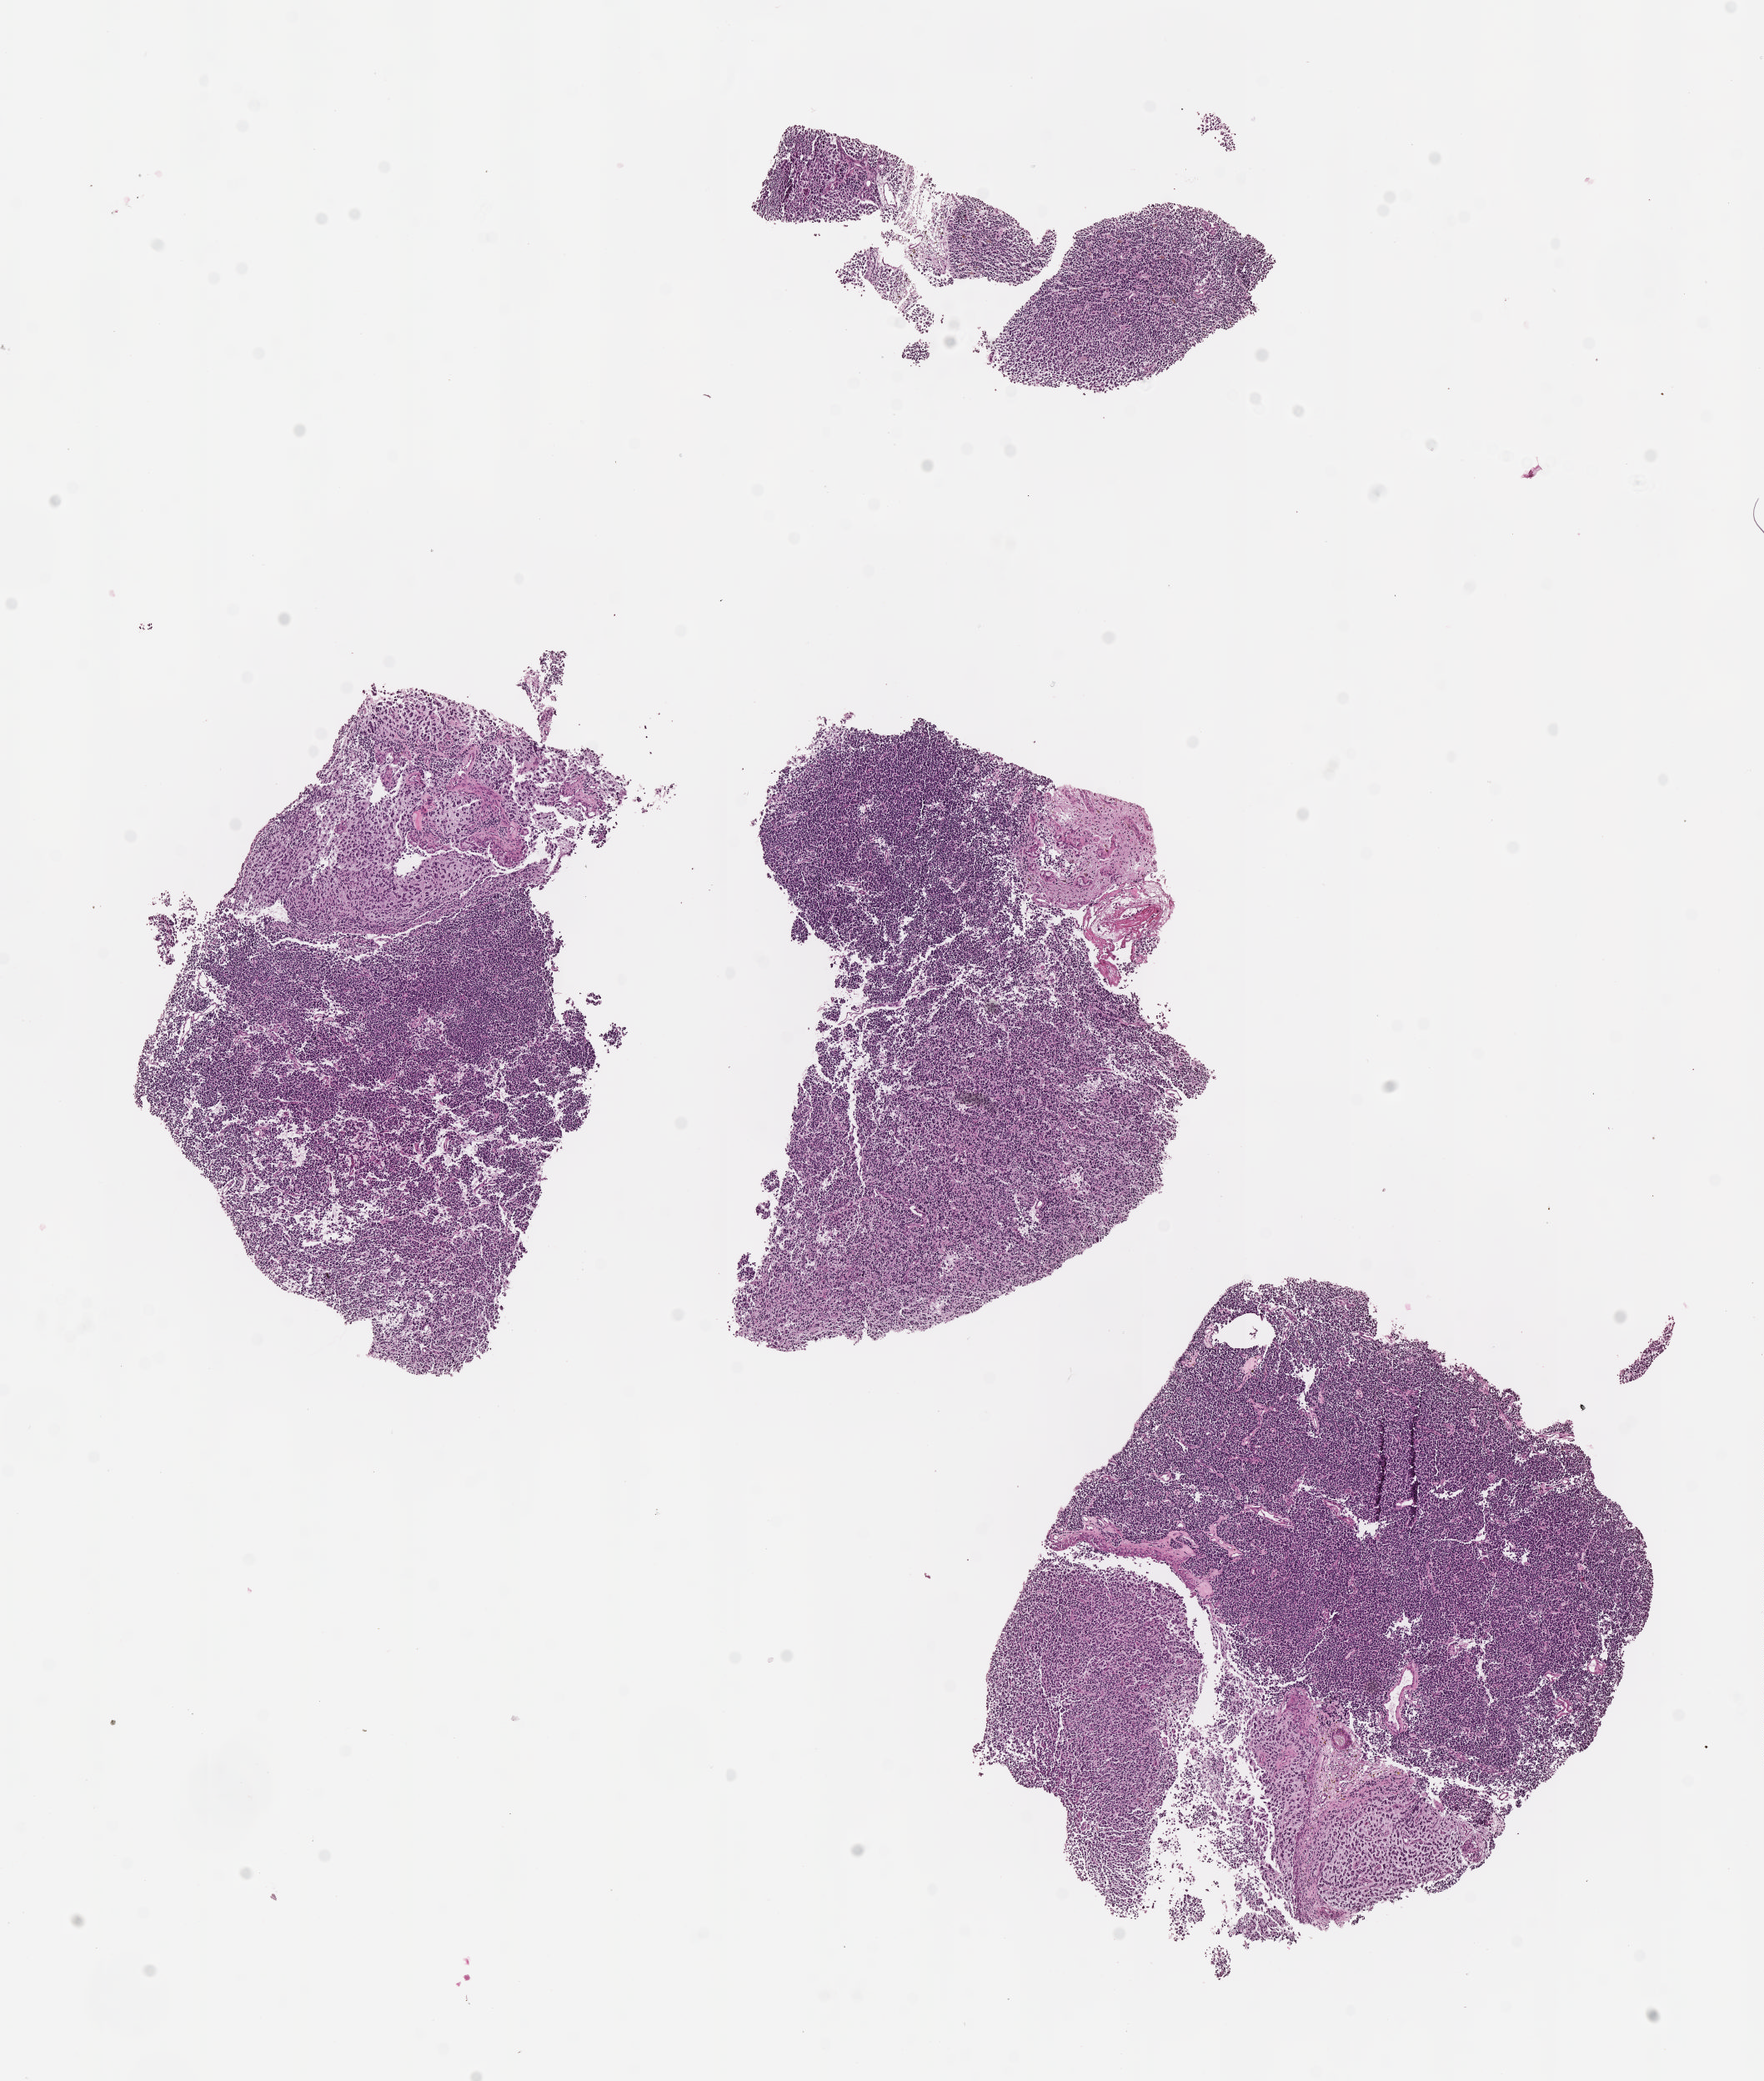
H&E whole-slide image, low-resolution overview of the scanned area, about 8.6 x 10.1 mm. Formalin-fixed paraffin-embedded (FFPE) diagnostic section. Brain, primary tumour sample. Female patient; age at initial diagnosis 73 years. Histologic grade: G3 (poorly differentiated).
Histologic diagnosis: Oligodendroglioma, anaplastic.